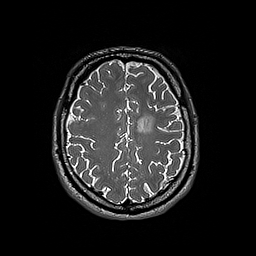
Brain MRI from a brain-tumour surgery series, one axial slice. Slice 61 of 192 in the series (ordered by position). 1 mm slice thickness. 256 × 256 image matrix, field of view 250 × 250 mm. Case-level facts recorded for this patient, not image findings: histopathology: Oligodendroglioma; WHO grade: 3; IDH mutation: yes.
Structures marked on this image (expert manual segmentation):
- tumour: box from (x=137, y=115) to (x=155, y=133) px